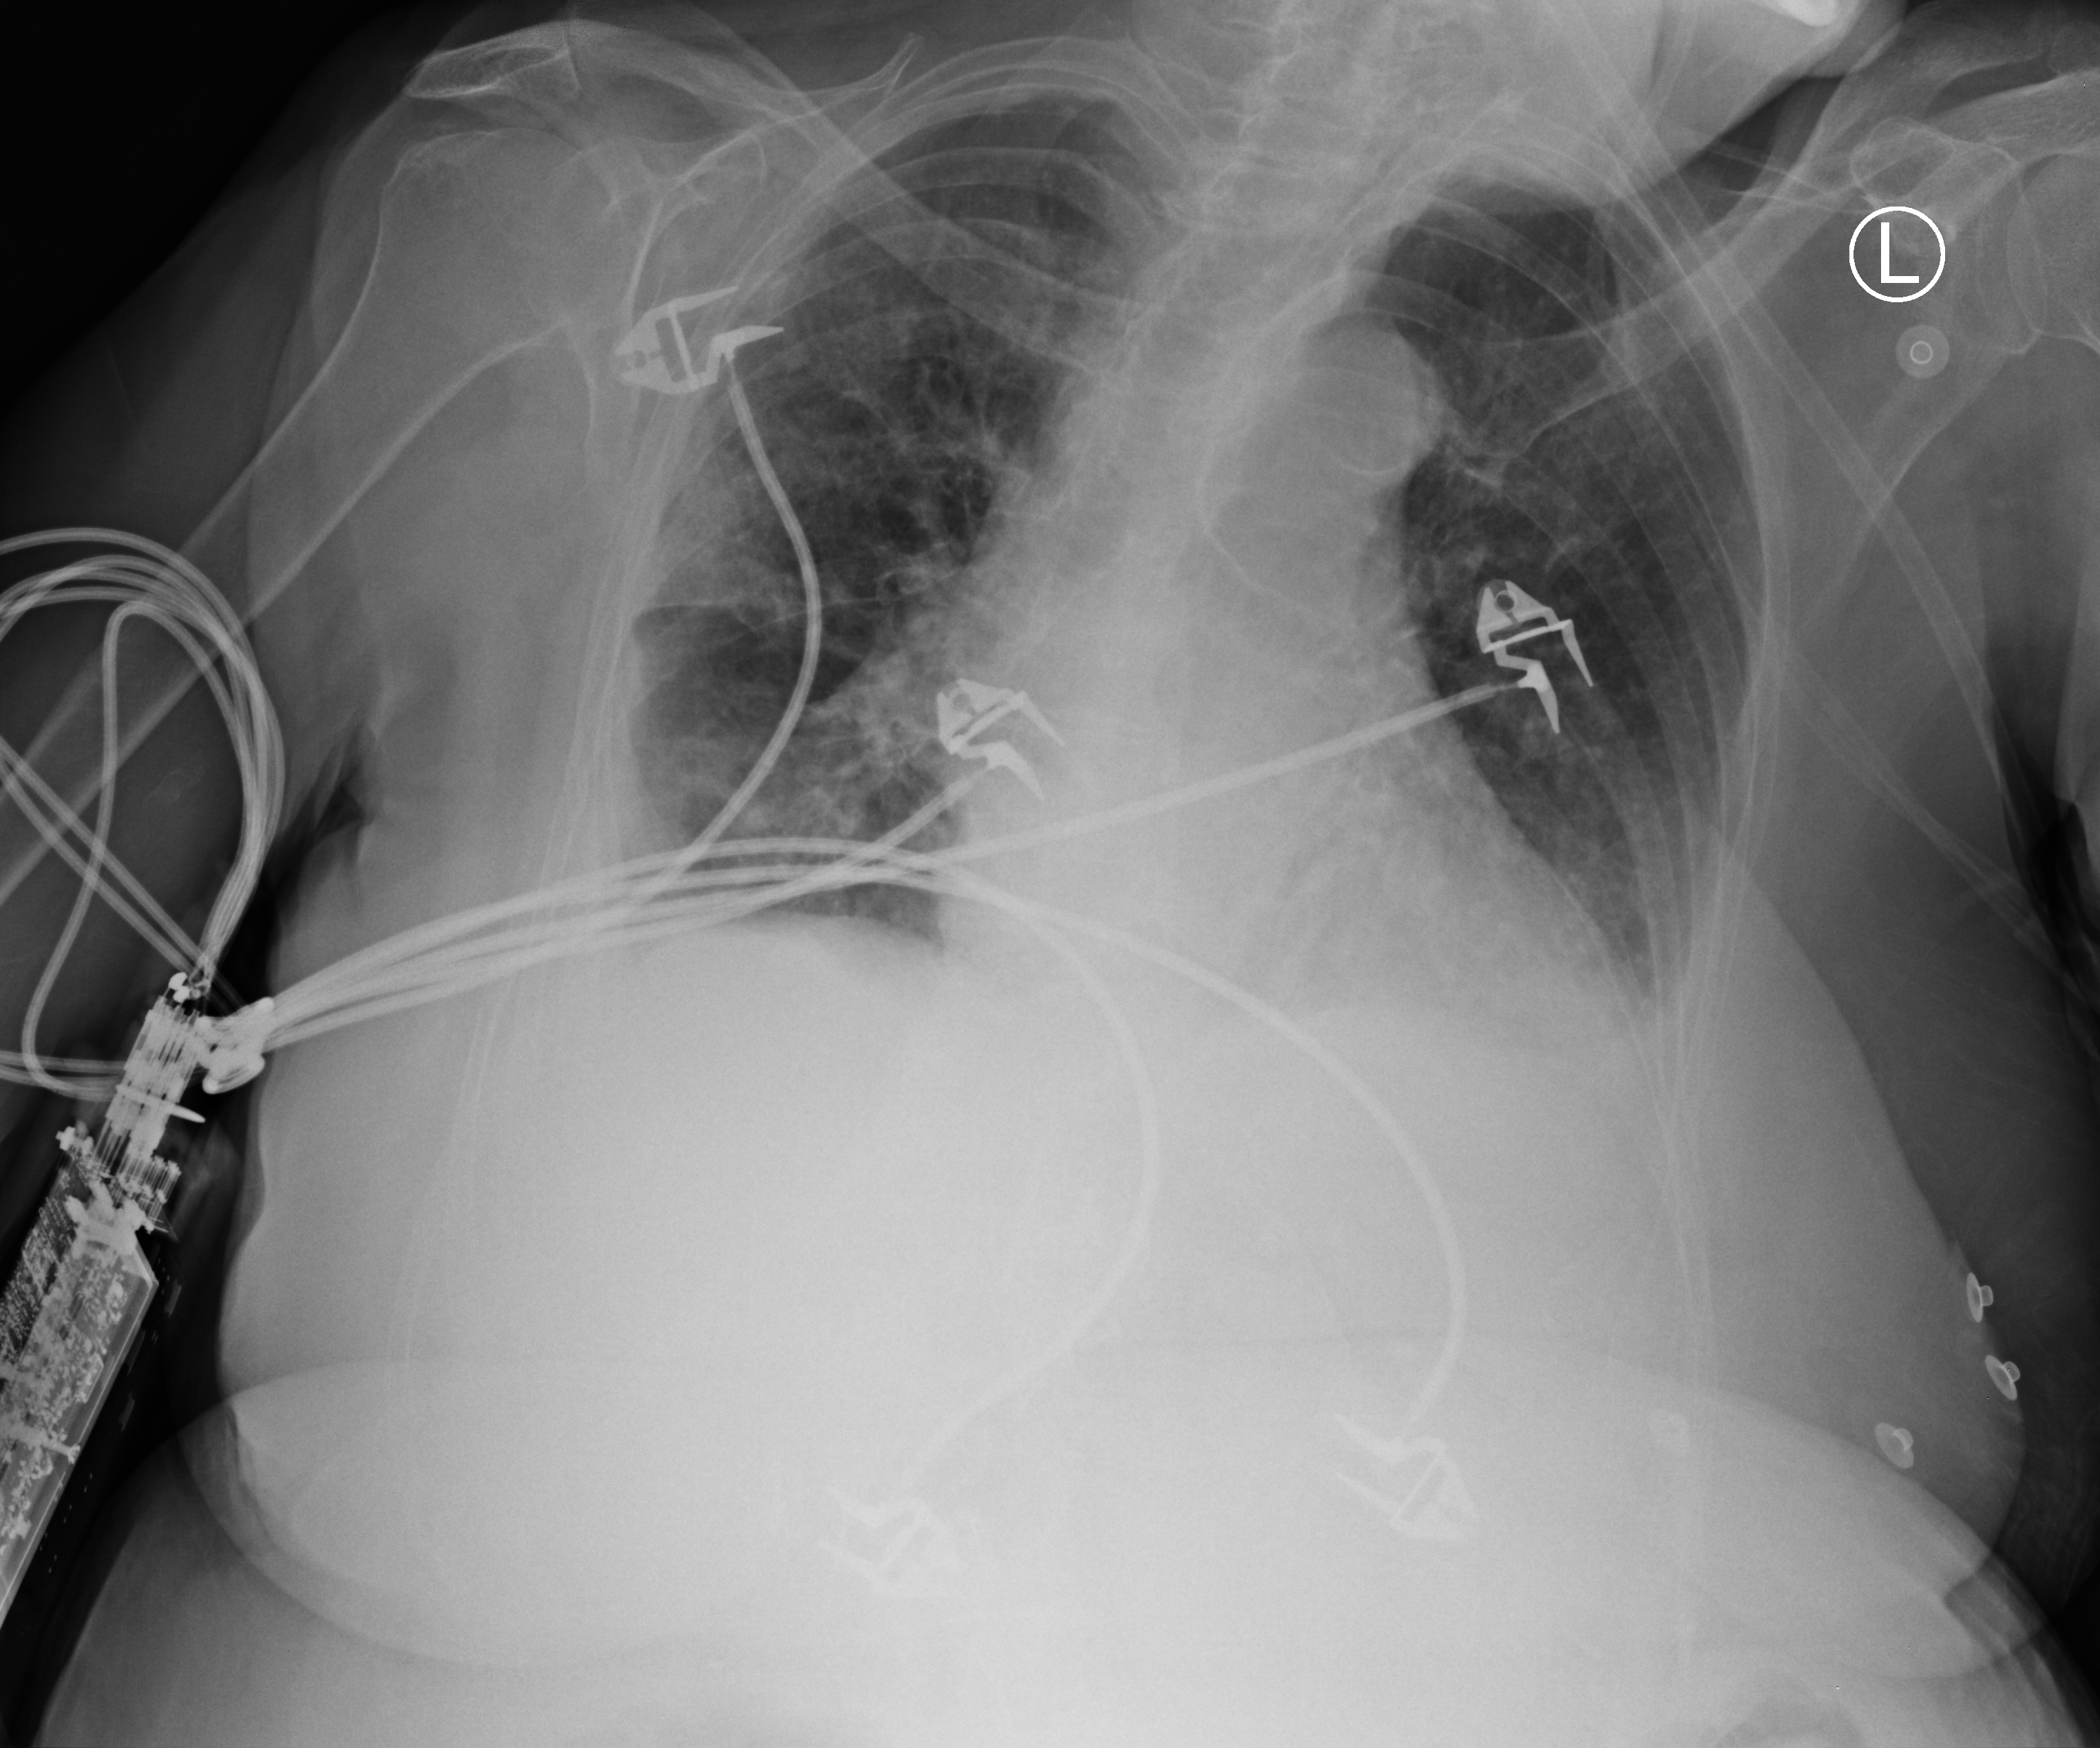
Portable chest radiograph, anteroposterior (AP) projection. Female patient hospitalised with COVID-19, age 75–90 years.
Admission-level facts for this patient (not findings on this image; timing relative to this image not recorded): admitted to intensive care during this hospital stay: no; mechanically ventilated during this hospital stay: no.